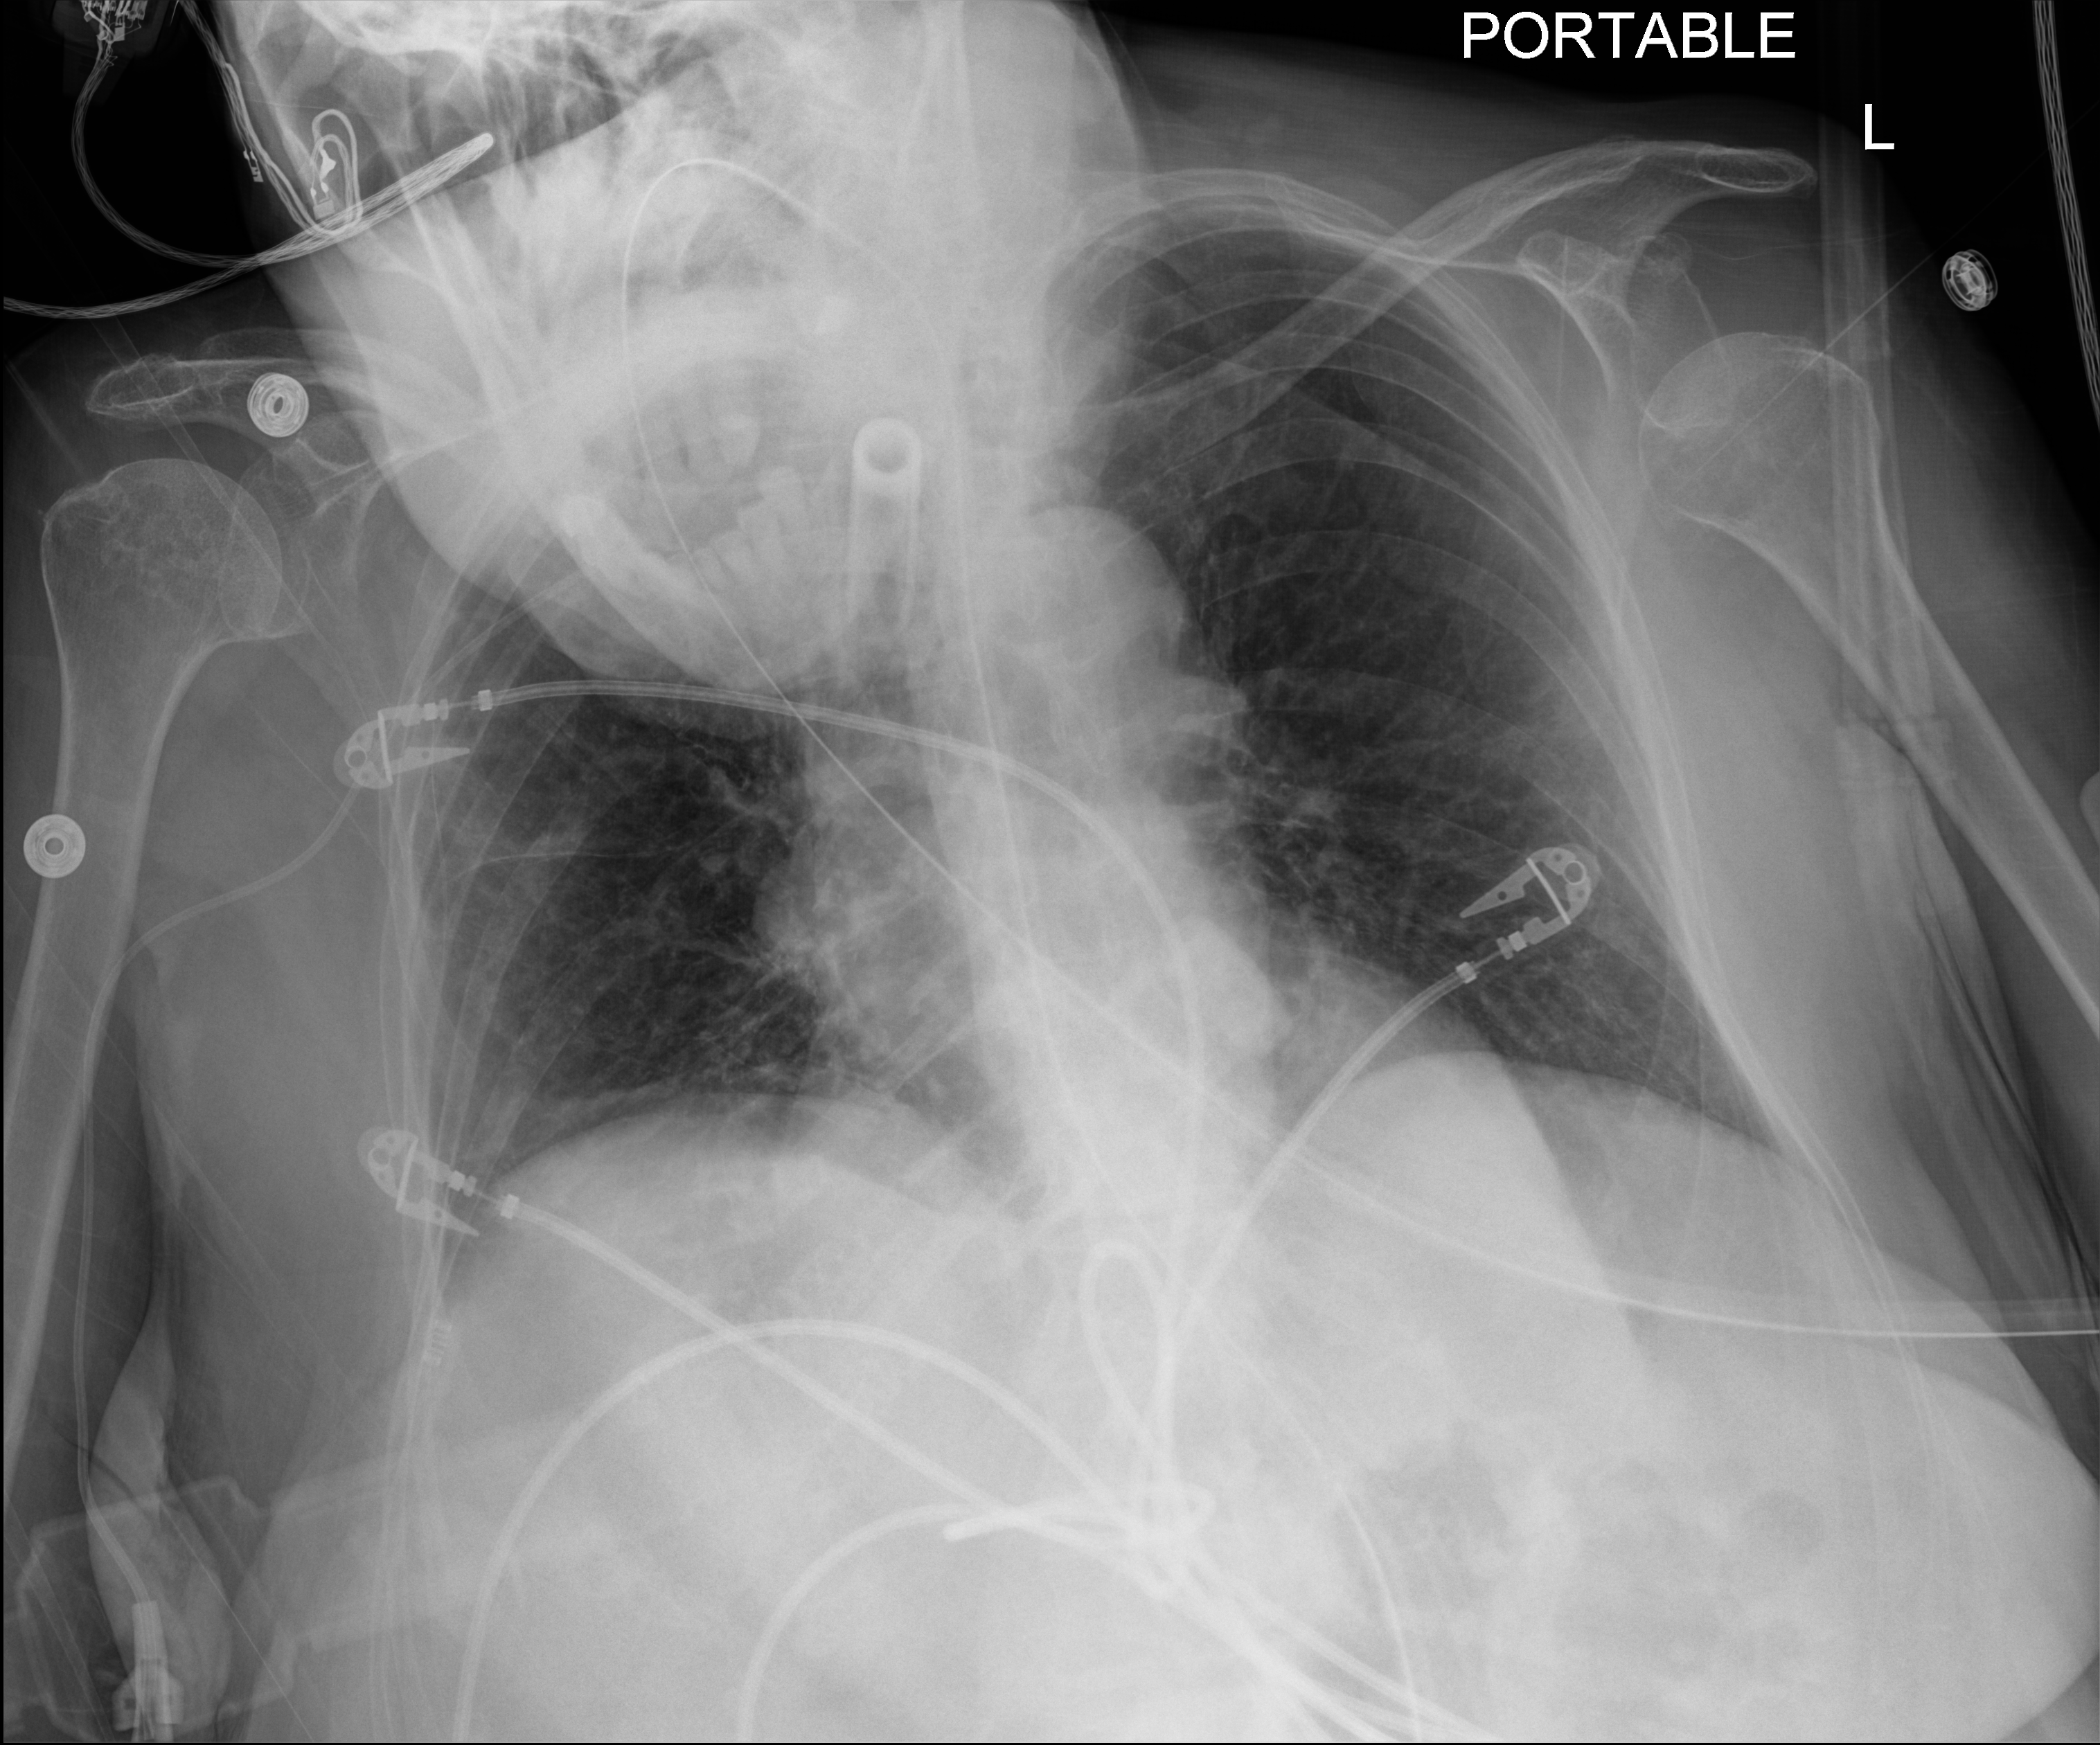
Bedside chest radiograph (digital radiography). Female patient hospitalised with COVID-19, age 75–90 years.
Admission-level facts for this patient (not findings on this image; timing relative to this image not recorded):
- chronic kidney disease (admission record): yes
- mechanically ventilated during this hospital stay: yes